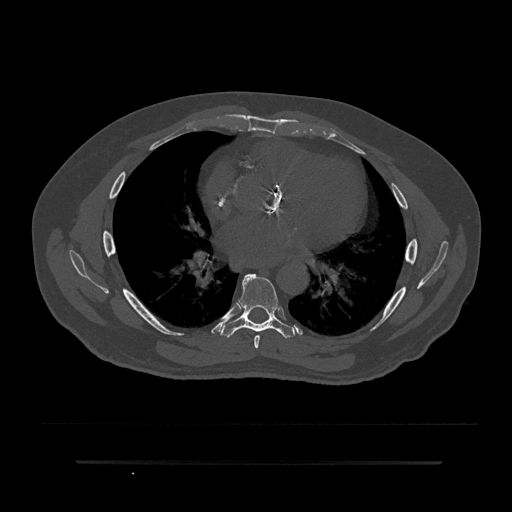
CT including the spine, one axial slice; reconstruction kernel Br40s/3; 120 kVp; bone window (W 1800 / L 400 HU); 0.5 mm slice thickness; 512 × 512 image matrix, field of view 464 × 464 mm. Male patient, age 59 years. From the clinical record (not read from this slice): primary cancer: bile ducts.
Structures marked on this image (semi-automatically segmented with operator editing):
- T6 vertebra: bounding box <254,335,260,349> (left, top, right, bottom; pixels)
- T7 vertebra: <220,274,295,338>